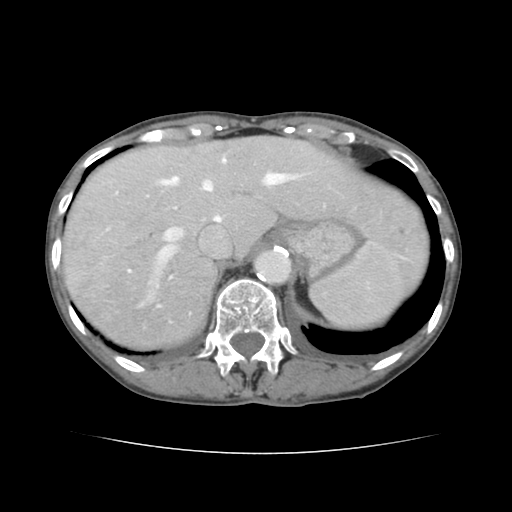
Contrast-enhanced abdominal CT, one axial slice. Position 110 of 136 along the scan axis. 120 kVp. Intravenous contrast given. Soft-tissue window (W 400 / L 40 HU). 2.5 mm slice thickness. 512 × 512 image matrix. Female patient, age 77 years. Case-level facts recorded for this patient, not image findings: diagnosis: colorectal cancer liver metastases, imaged before liver resection; multiple liver metastases: yes; largest metastasis: 3 cm; disease in both lobes: no.
Annotated regions visible in this slice (outlined manually by an expert reader):
- hepatic veins: bounding box [x1, y1, x2, y2] px = [102, 159, 287, 266]
- liver: [62, 137, 427, 349]
- planned liver remnant (the part of the liver to remain after resection): [166, 137, 427, 279]
- portal vein (with intrahepatic branches): [170, 184, 338, 278]